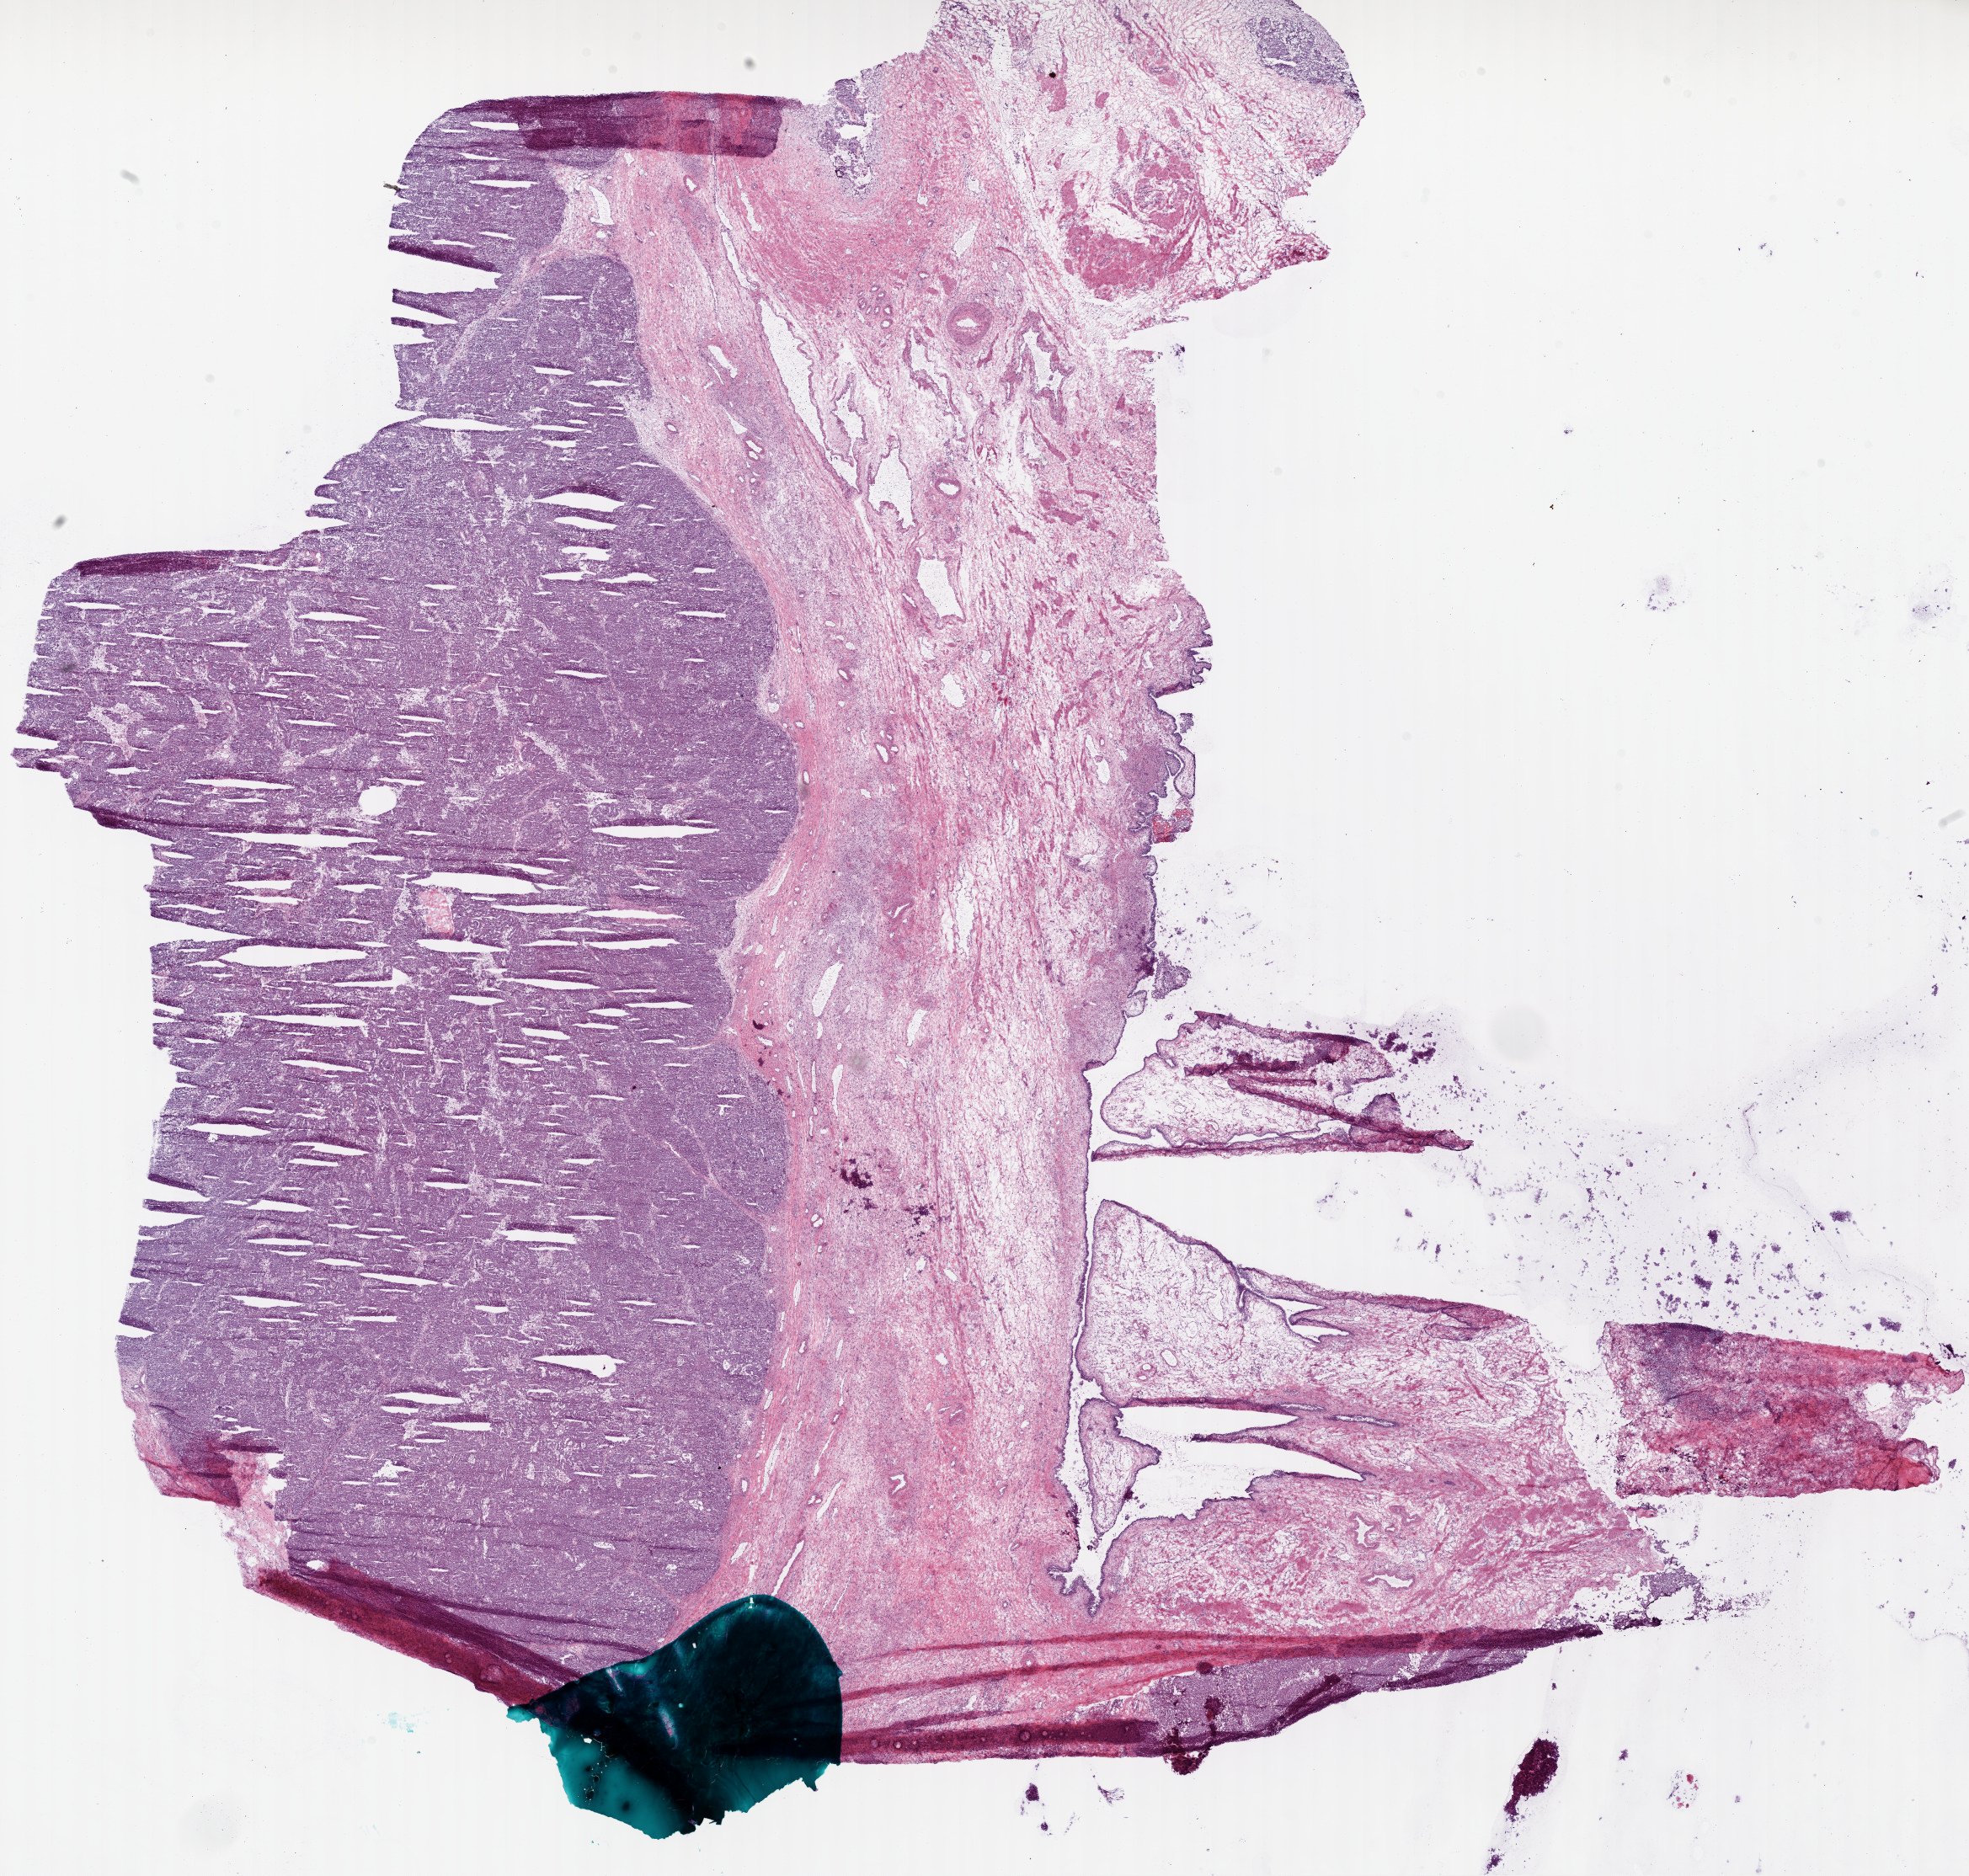
H&E whole-slide image, shown as a low-resolution overview of the whole scanned area (about 18.9 x 18.0 mm); frozen section; ovary, primary tumour sample. Female patient; age at initial diagnosis 73 years. Histologic grade: G3 (poorly differentiated). Pathologist review of this section (percent, as recorded): tumour cells 50%, tumour nuclei 95%, normal cells 10%, stromal cells 40%, necrosis 0%.
Laterality: bilateral. FIGO stage: IIIC. Histologic diagnosis: Serous cystadenocarcinoma, NOS.